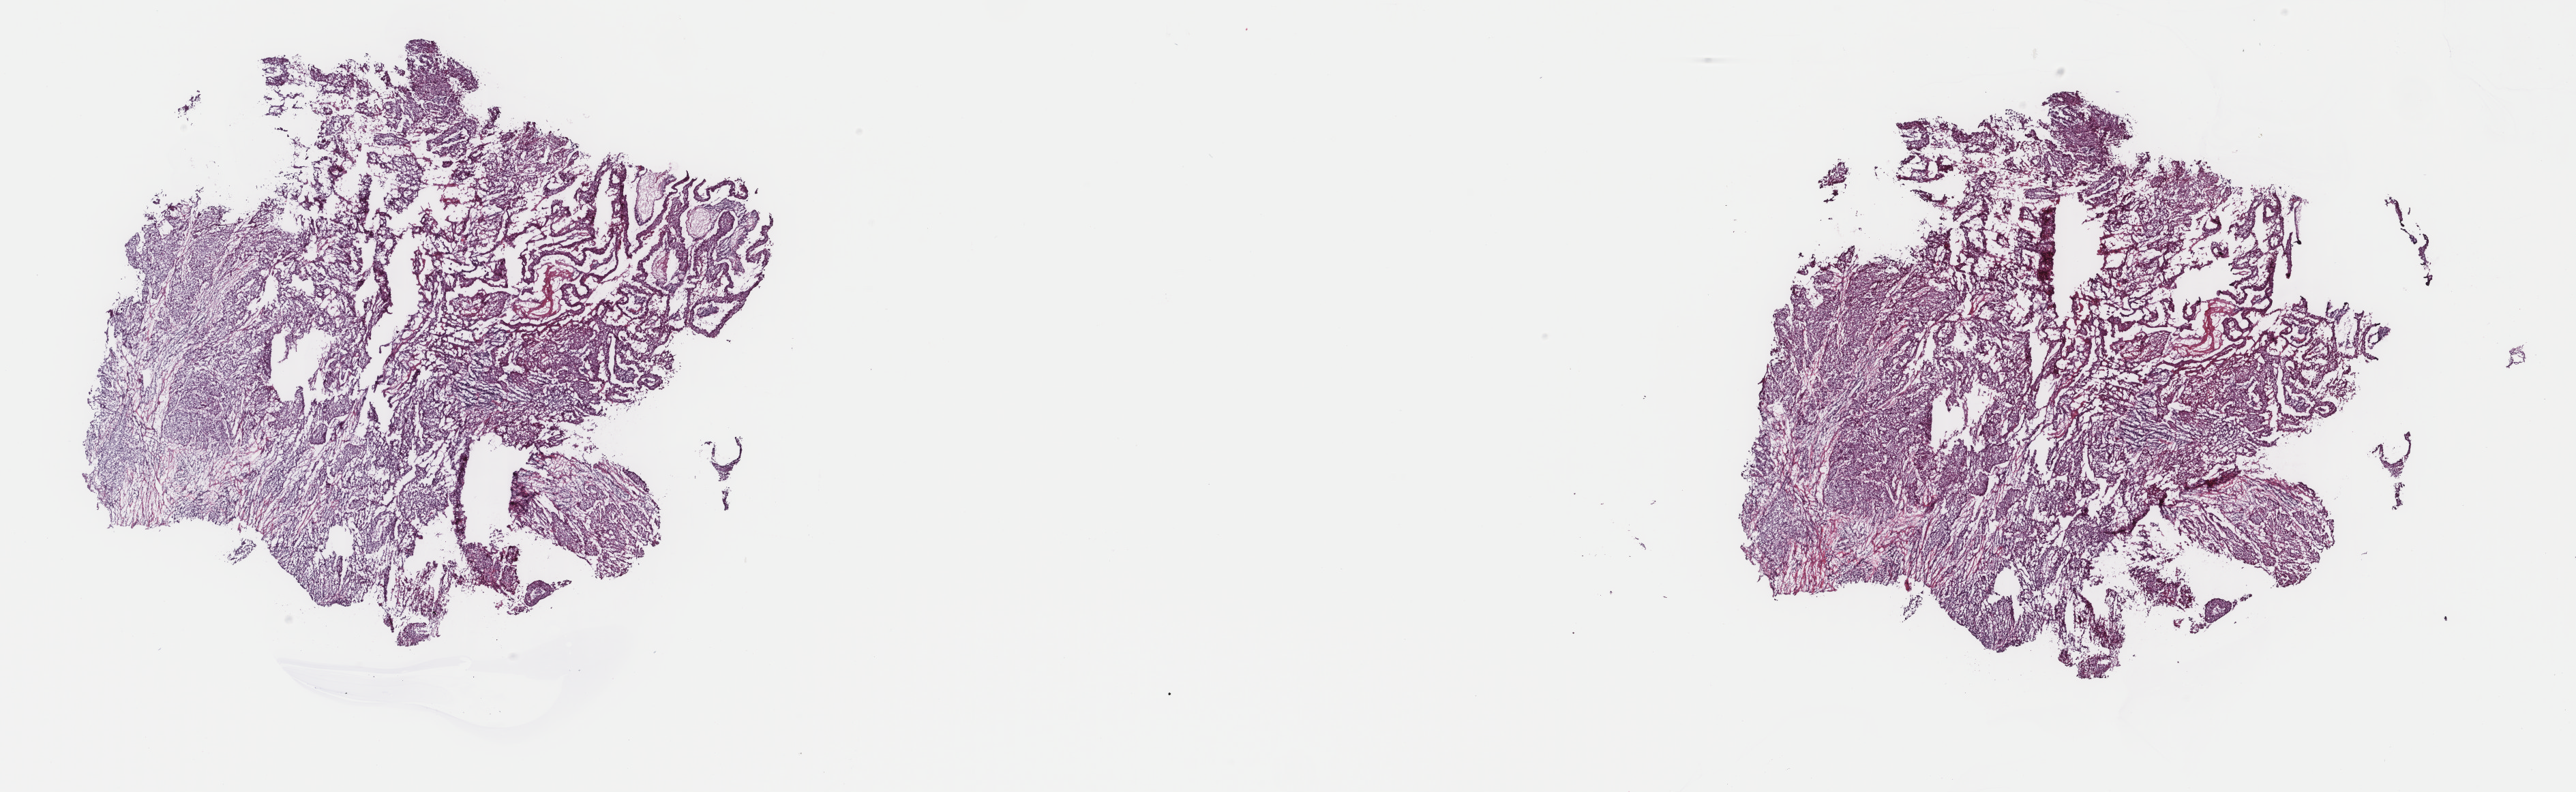
H&E whole-slide image — whole scanned area (about 30.0 x 9.2 mm, acquisition: 40x scan) shown as a low-resolution overview, frozen section from the top of the tissue portion, primary tumour sample from the cervix. Female patient; age at initial diagnosis 69 years. Histologic grade: G3 (poorly differentiated). Pathologist review of this section (percent, as recorded): tumour cells 100%, tumour nuclei 90%, normal cells 0%, stromal cells 0%, necrosis 0%. Inflammatory infiltration, as recorded: lymphocyte infiltration 2%, monocyte infiltration 0%, neutrophil infiltration 0%.
Diagnosis: Squamous cell carcinoma, NOS (cervix uteri). Lymph nodes positive (case pathology): 0 of 17 examined. FIGO stage: IB2.